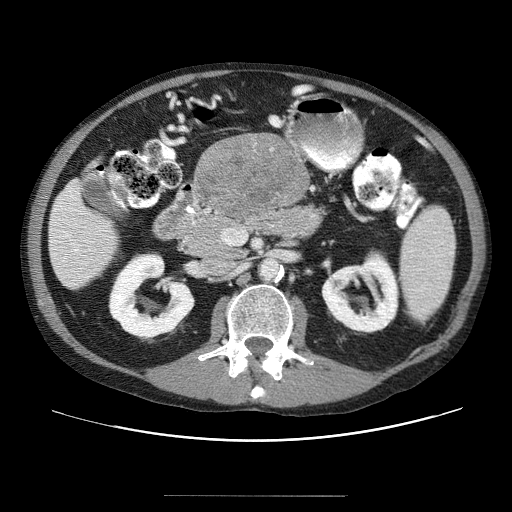
Contrast-enhanced abdominal CT (liver protocol), one axial slice. Slice 8 of 69 in the series (ordered by position). 120 kVp. Soft-tissue window (W 400 / L 40 HU). 512 × 512 image matrix. Case-level facts recorded for this patient, not image findings: diagnosis: hepatocellular carcinoma (patient treated with transarterial chemoembolisation; whether this scan precedes or follows treatment is not stated here); TNM stage (as recorded): Stage-IVB; Child-Pugh class: B.
Structures marked on this image (semi-automatic segmentation, software-assisted and operator-edited):
- liver parenchyma outside the tumour (the mass and vessels are separate outlines, so this box may not span the whole liver): box from (x=48, y=187) to (x=284, y=286) px
- mass: (x=193, y=137)–(x=309, y=217)
- liver vessels: (x=55, y=211)–(x=104, y=271)